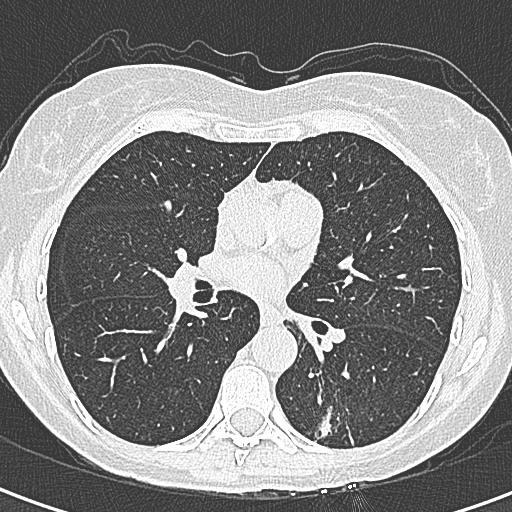
Chest CT (low-dose screening protocol), one axial image. Baseline screening round. Lung window (W 1500 / L -600 HU). Slice 143 of 328 in the series. Female participant, aged 58 years at enrolment. Former smoker at enrolment.
Expert reader's lesion annotation, bounding box [x1, y1, x2, y2] px = [299, 385, 369, 457]. The screening reader recorded 2 non-calcified nodules or masses ≥4 mm on this exam; which of them this box marks is not recorded. Official screen result: positive, change unspecified: nodule(s) >= 4 mm or enlarging nodule(s), mass(es), or other non-specific abnormalities suspicious for lung cancer. Lung cancer was diagnosed 22 days after this screen: adenocarcinoma, NOS, left lower lobe, moderately differentiated (G2), stage IA (AJCC 6th edition), 25 mm at pathology.